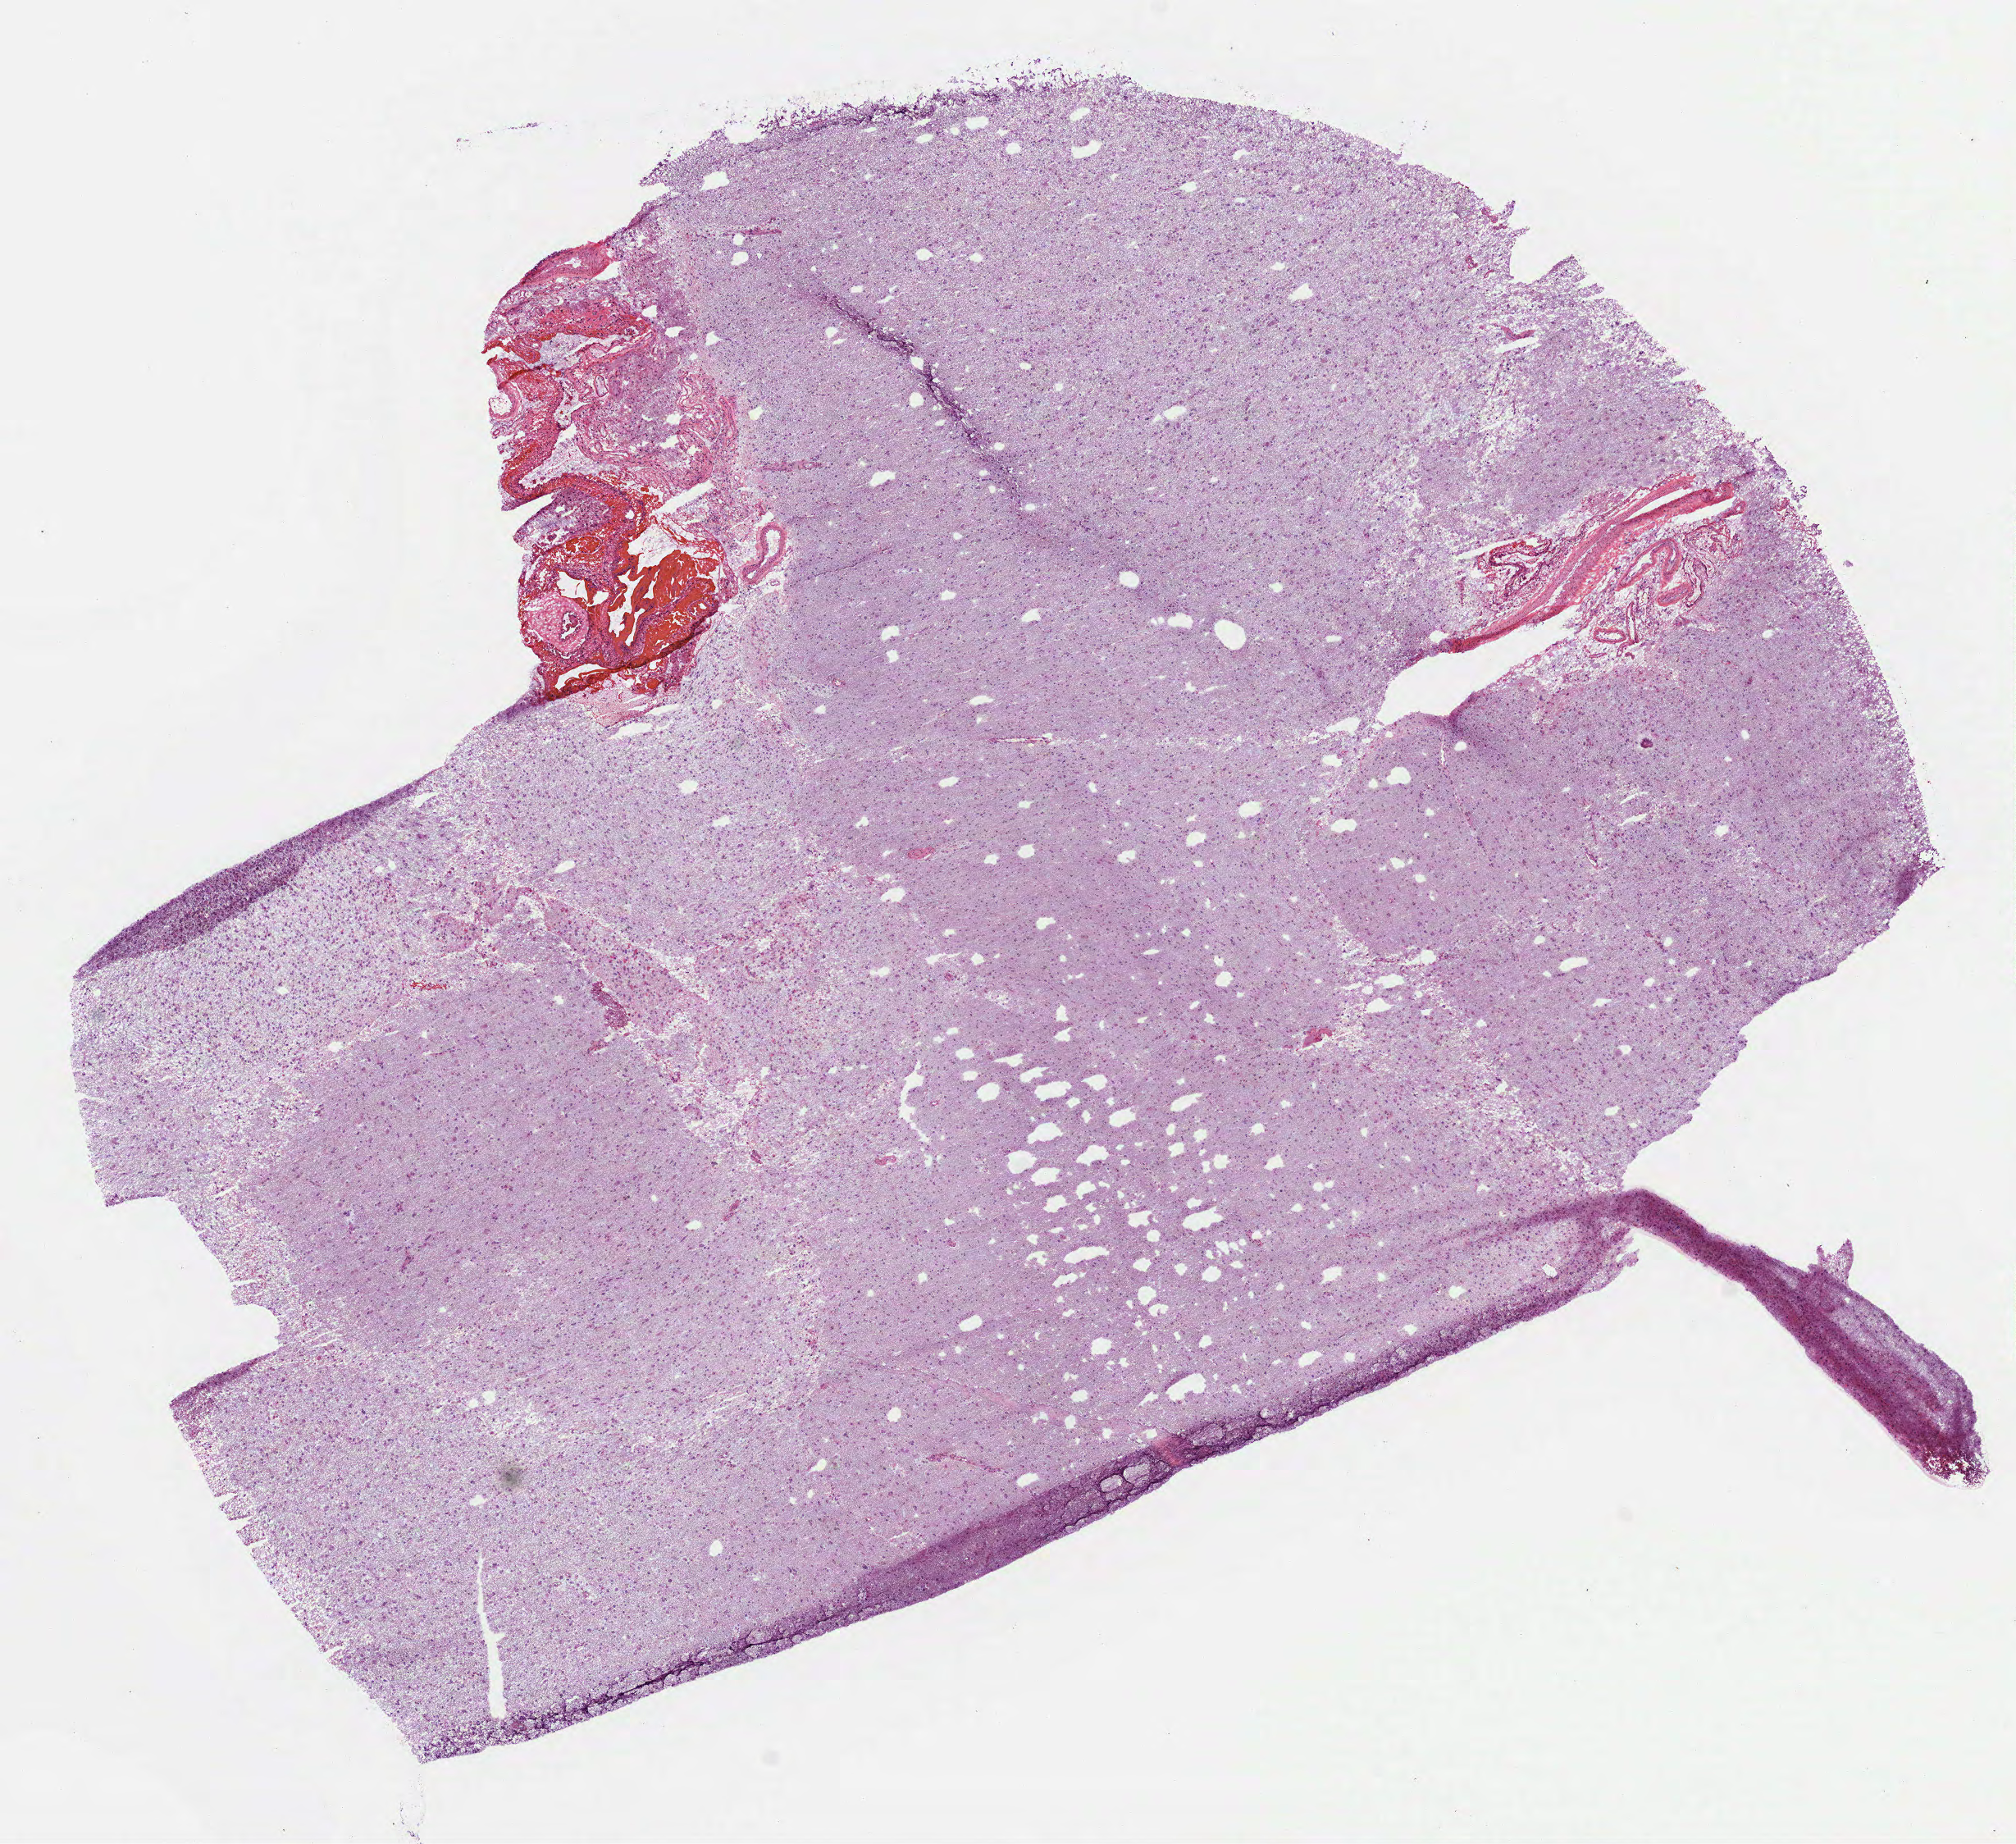
Digitized H&E tissue section (whole slide) — low-resolution overview of the scanned area, about 9.9 x 9.1 mm, frozen section, primary tumour sample from the brain. Patient: female, age at initial diagnosis 41 years. Histologic grade: G3 (poorly differentiated). Slide review estimates, as recorded: tumour cells 100%, tumour nuclei 60%, normal cells 0%, stromal cells 0%, necrosis 0%.
* diagnosis: Oligodendroglioma, anaplastic